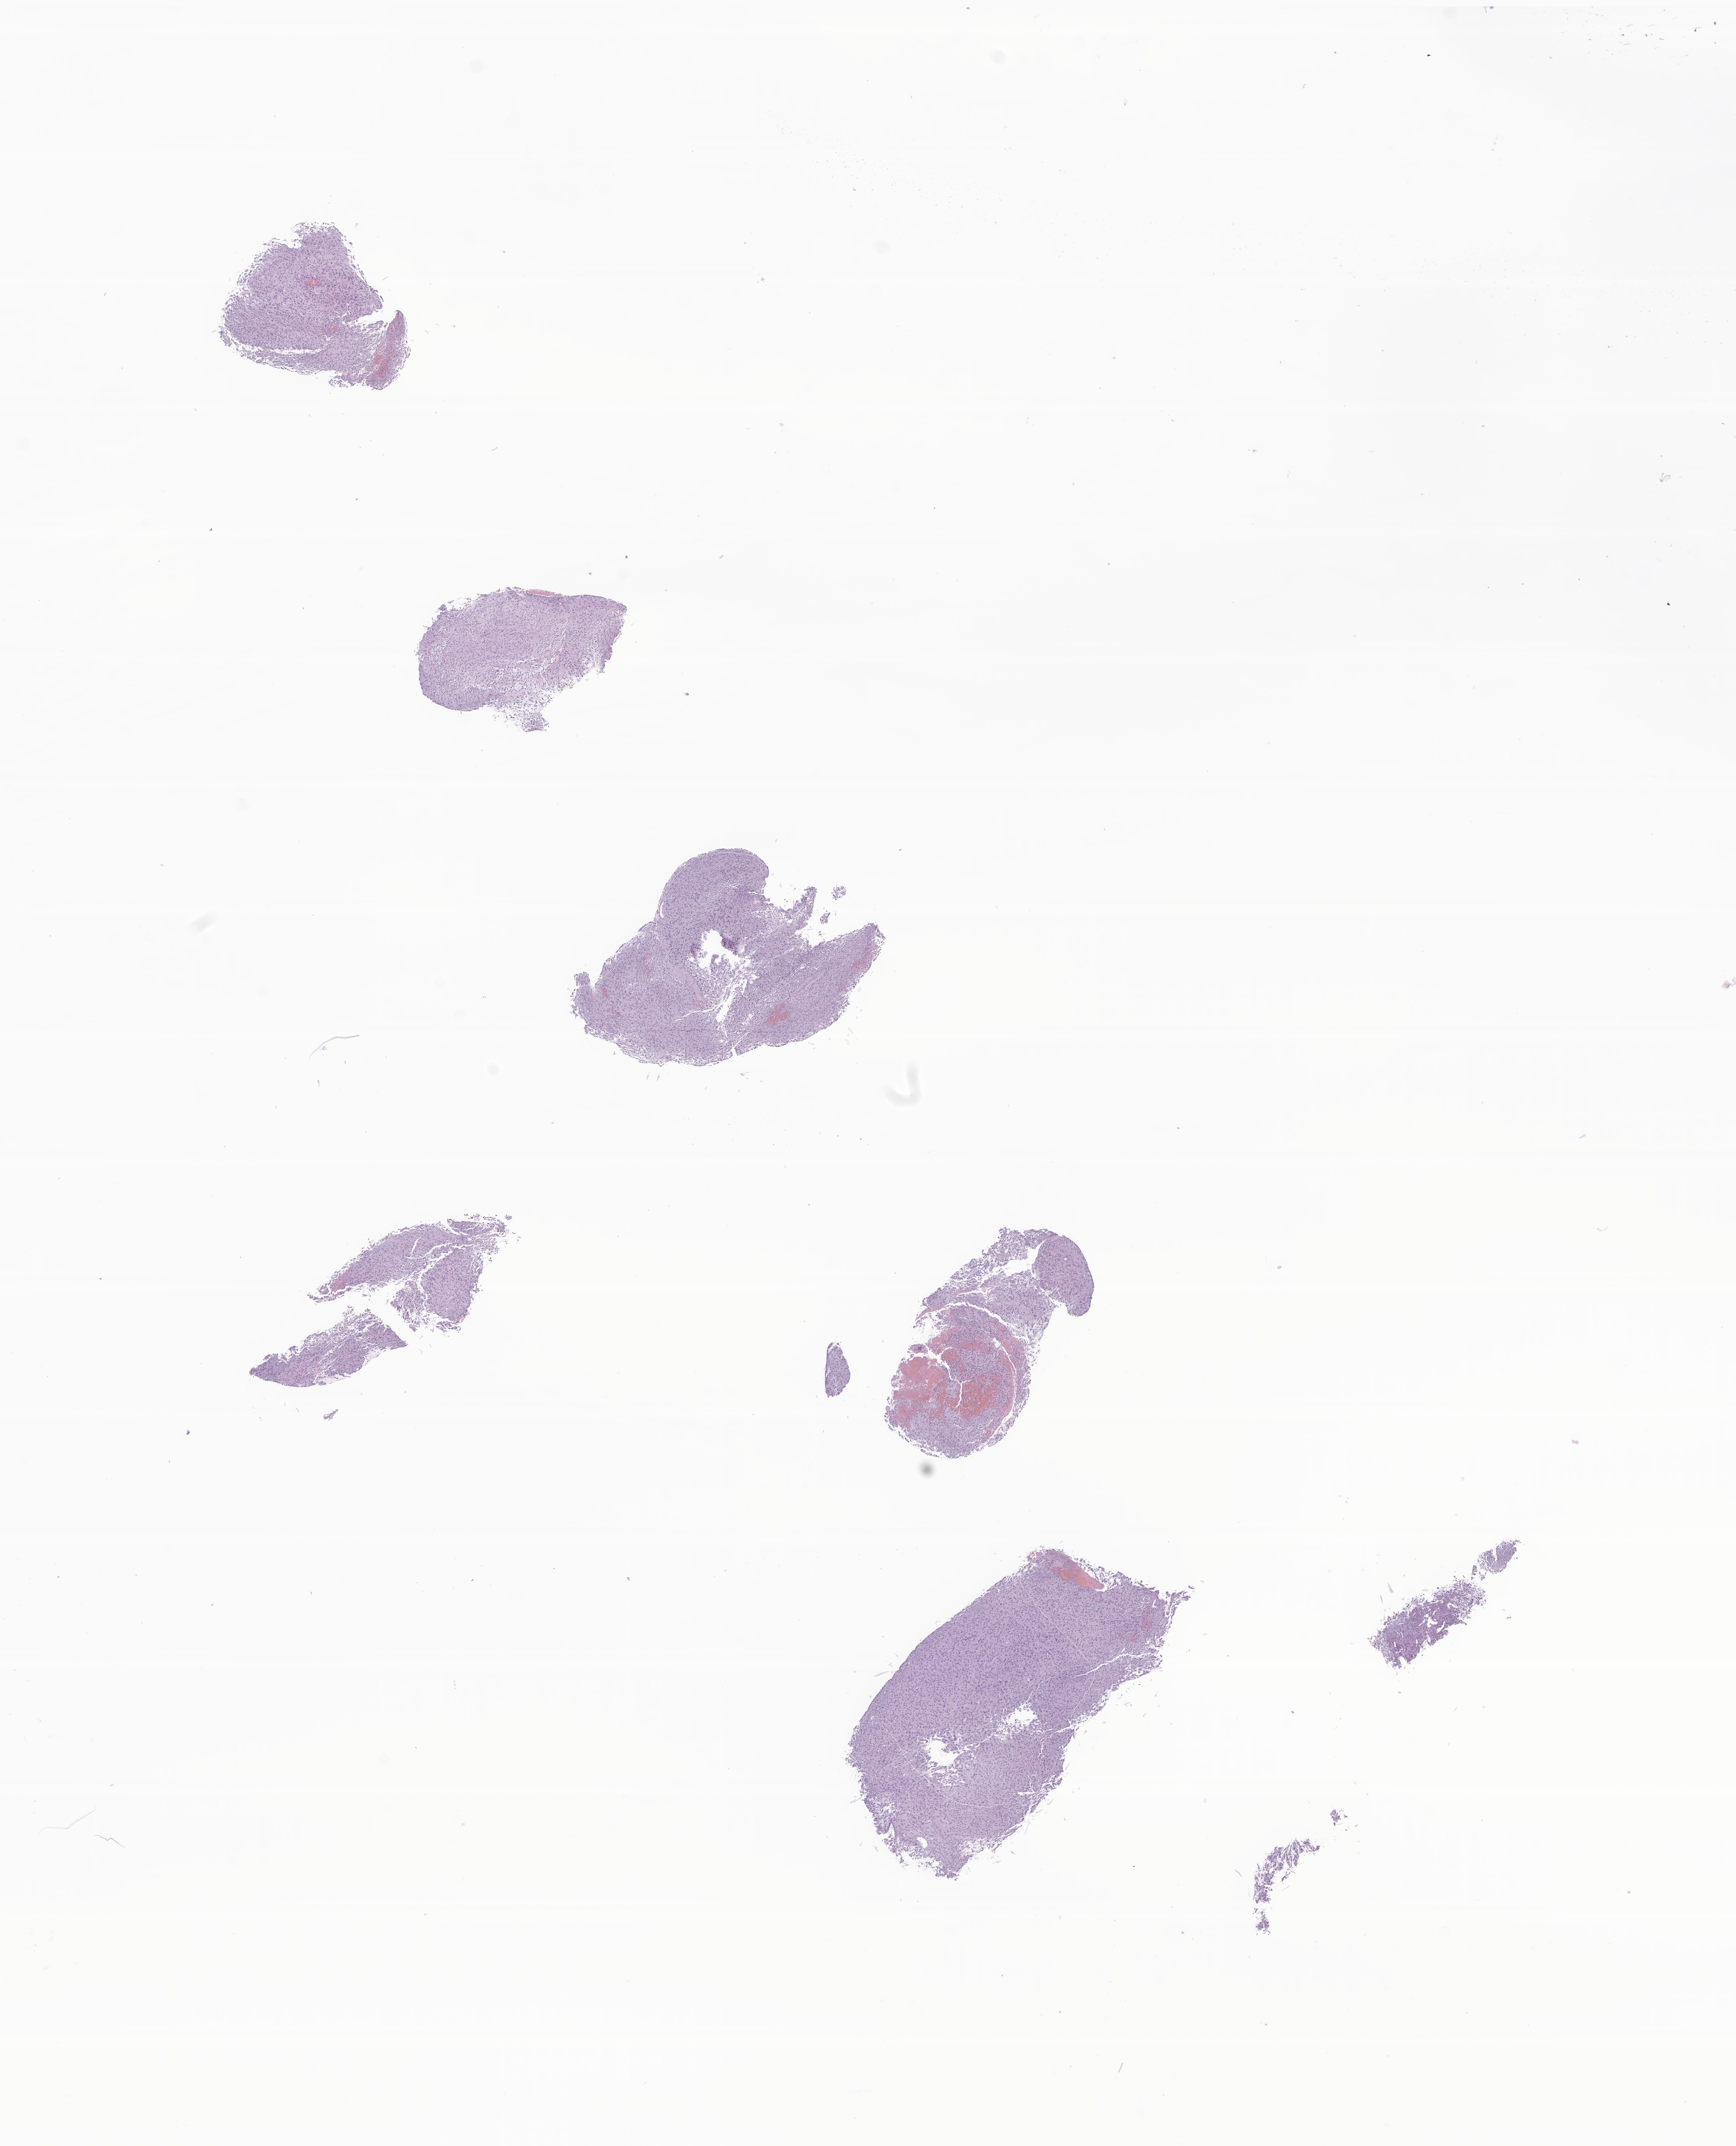
H&E whole-slide image of tumor tissue from the brain, shown as a low-resolution overview of the whole scanned area (about 14.7 x 18.2 mm); formalin-fixed paraffin-embedded section. Patient female; age 170 months (14 years 2 months).
Diagnosis: Neoplasm, malignant.